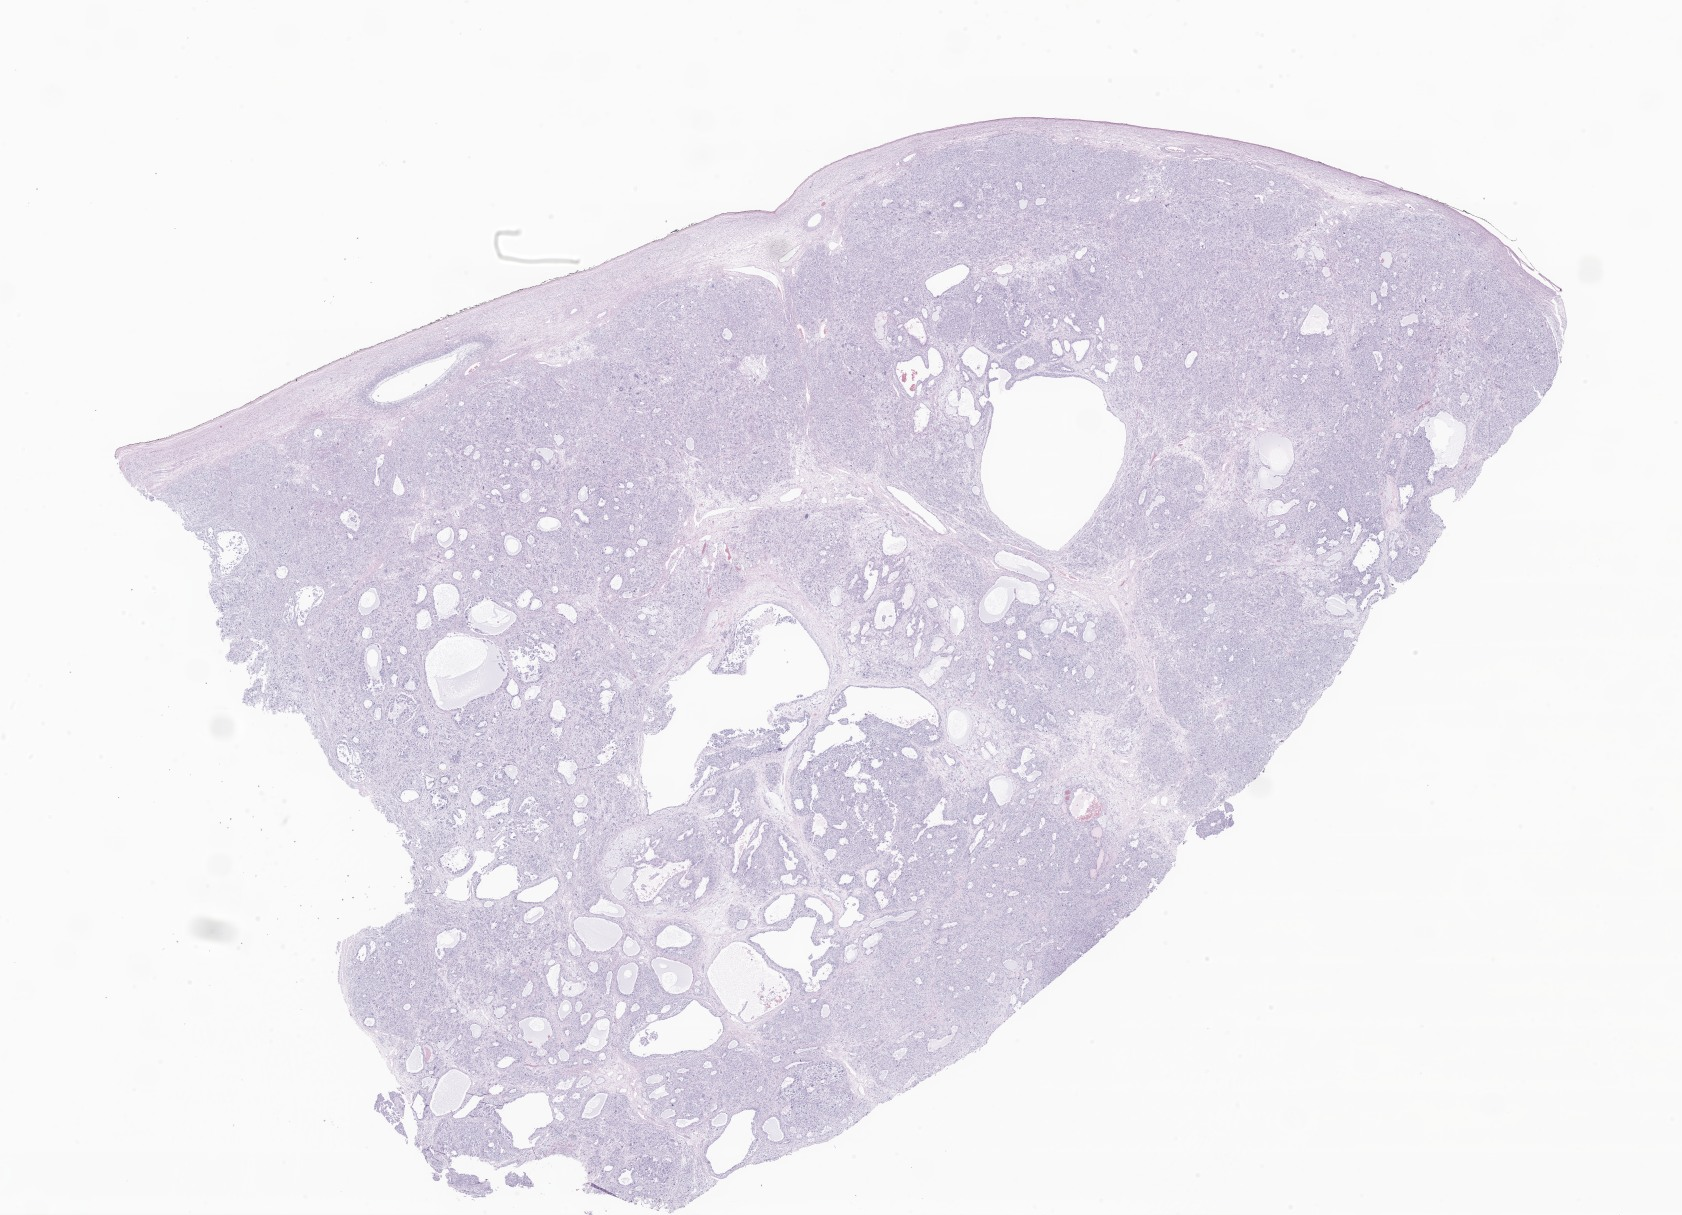
Whole-slide image, hematoxylin and eosin (H&E) stain of tumor tissue from the ovary — shown as a low-resolution overview of the whole scanned area (about 28.4 x 20.5 mm), FFPE section. Patient female; age 68 months (5 years 8 months).
Recorded diagnosis: Sex cord-gonadal stromal tumor, NOS.